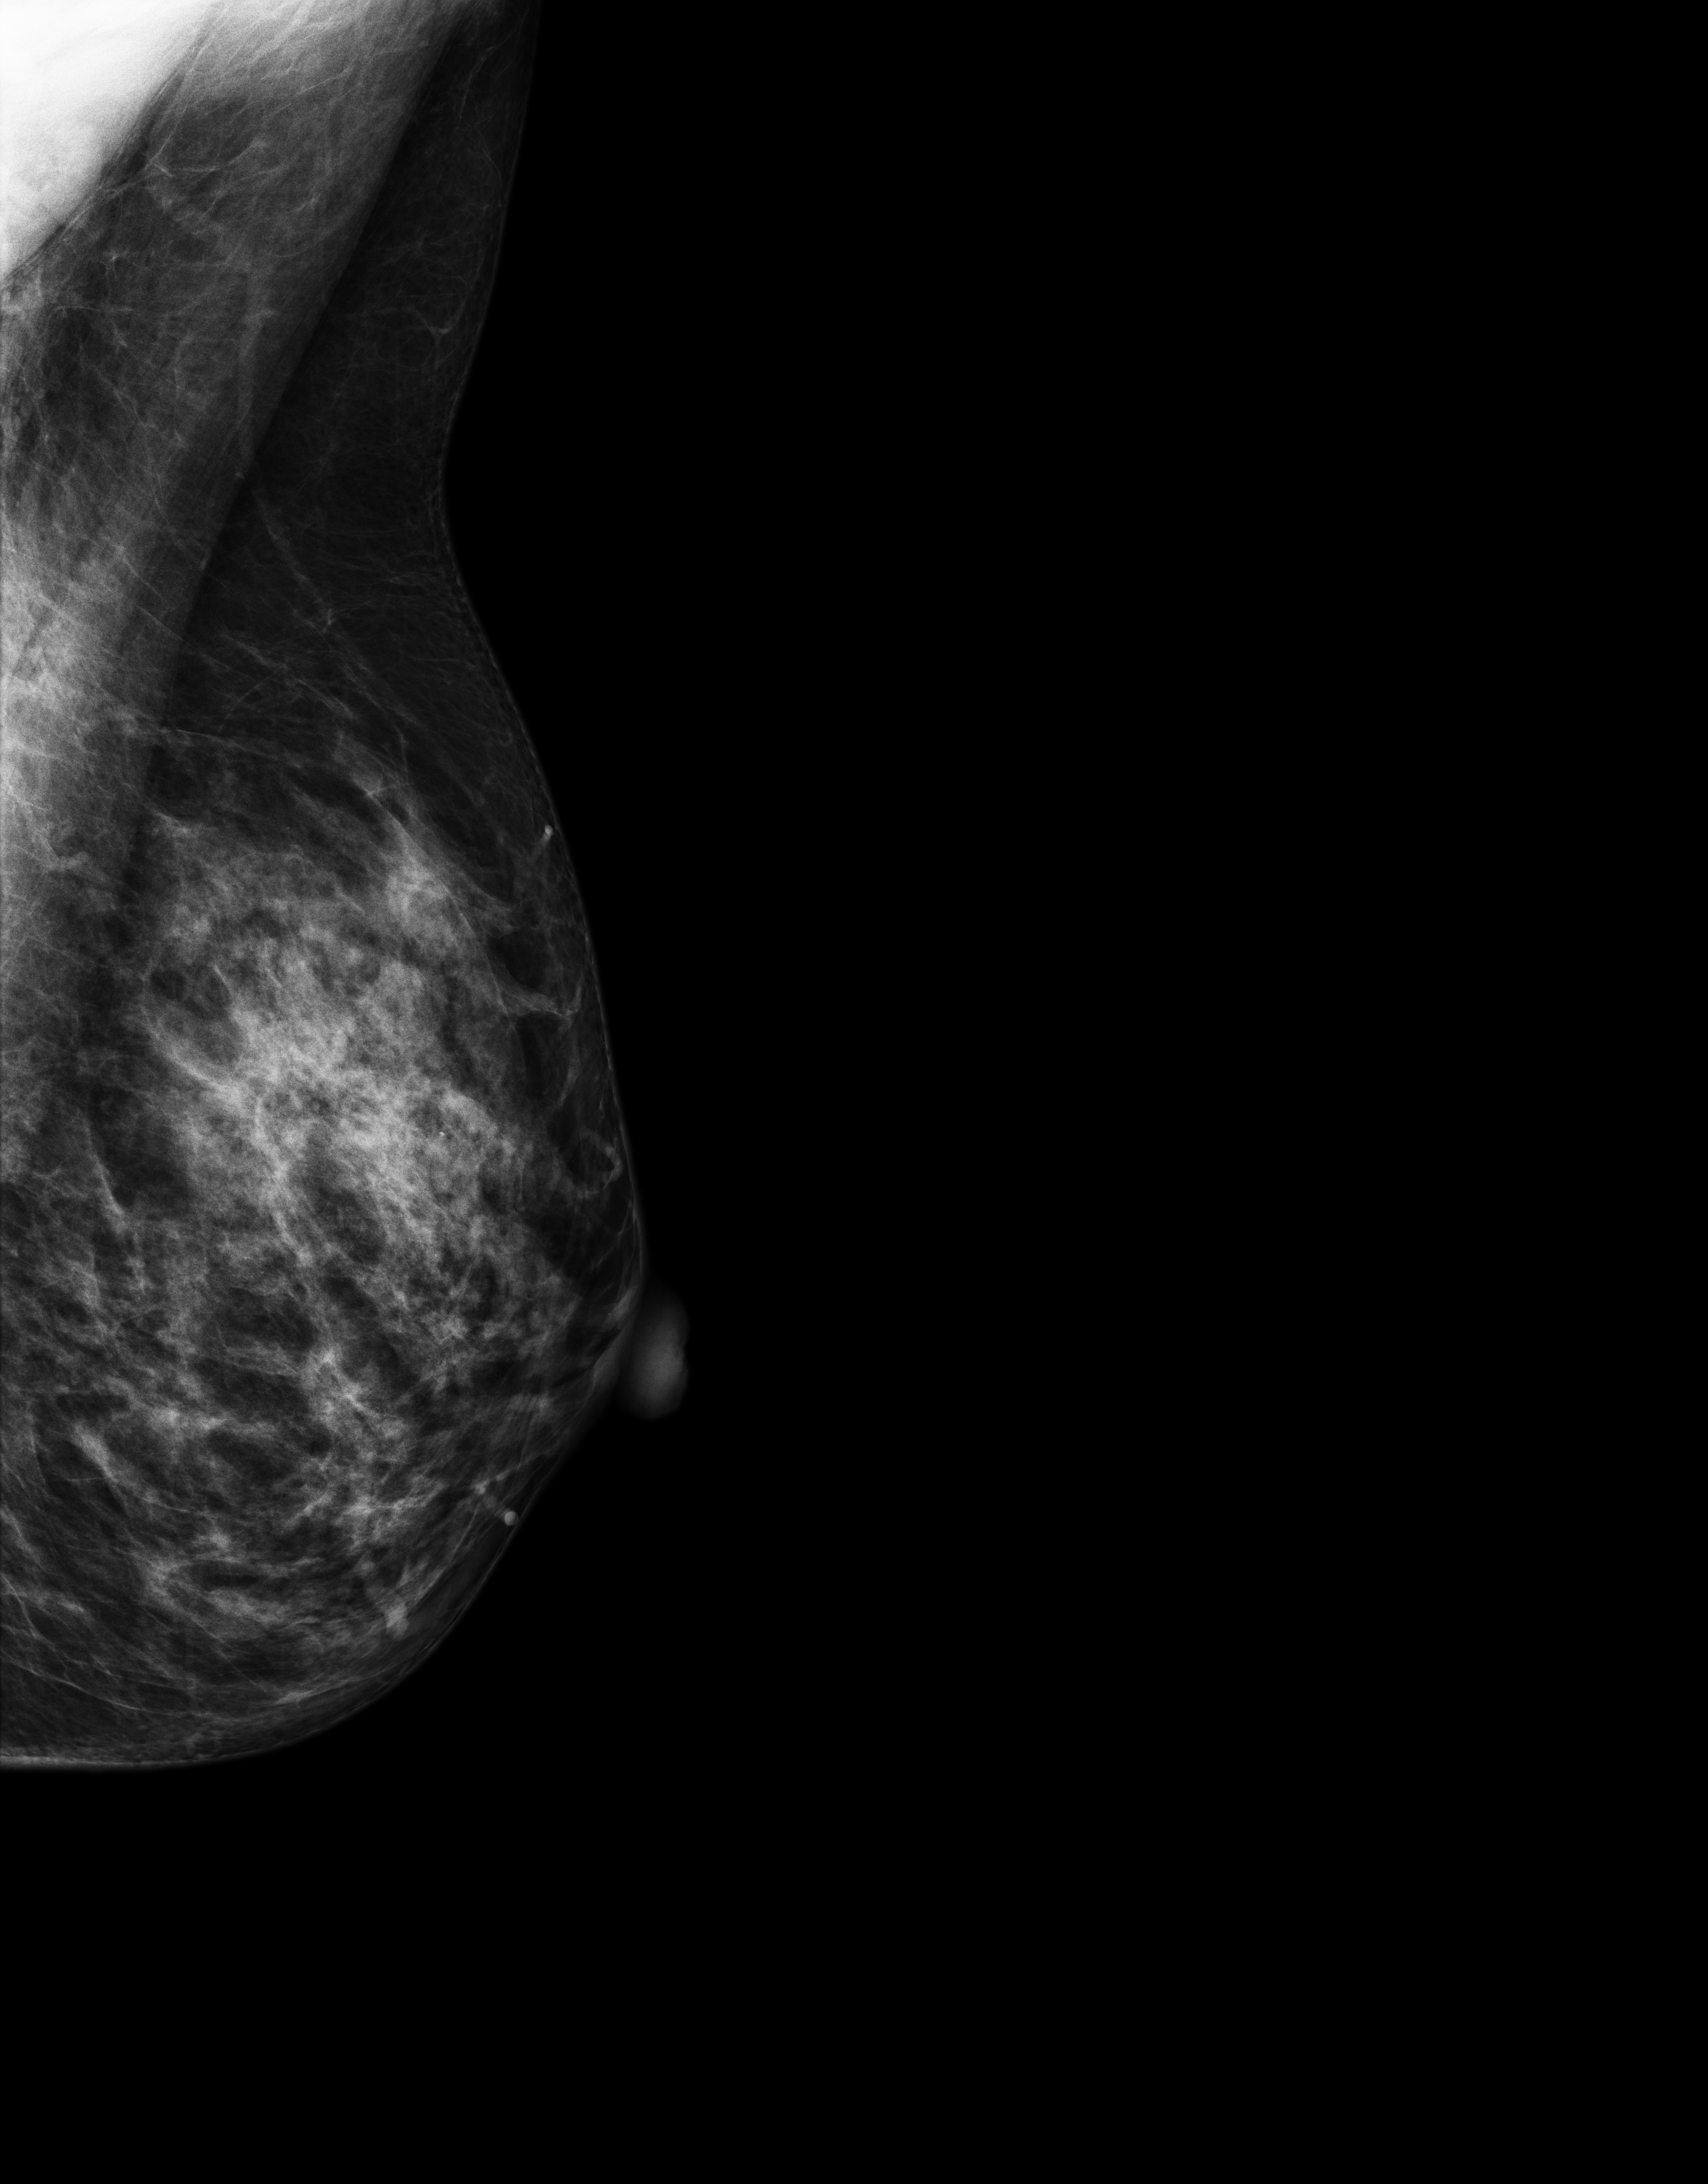
Annual screening mammography examination; system: Senographe Essential ADS_56.21.3. Patient aged 43 years (female).
Image type: full-field digital mammogram. Breast: left. Projection: MLO view.